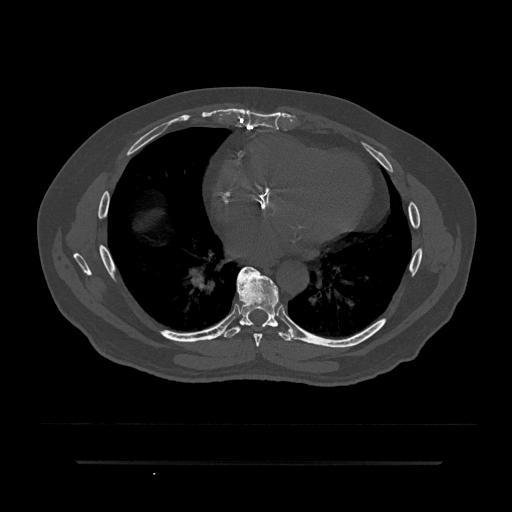
CT including the spine, one axial slice. Slice 450 of 797 in the series (ordered by position). Reconstruction kernel Br40s/3. Bone window (W 1800 / L 400 HU). 512 × 512 image matrix, field of view 464 × 464 mm. Male patient, age 59 years. Case-level facts recorded for this patient, not image findings: primary cancer: bile ducts.
Outlined on this slice (semi-automatic segmentation, software-assisted and operator-edited):
- T7 vertebra: bounding box (x1, y1, x2, y2) in pixels: (236, 266, 262, 347)
- T8 vertebra: (222, 269, 295, 341)